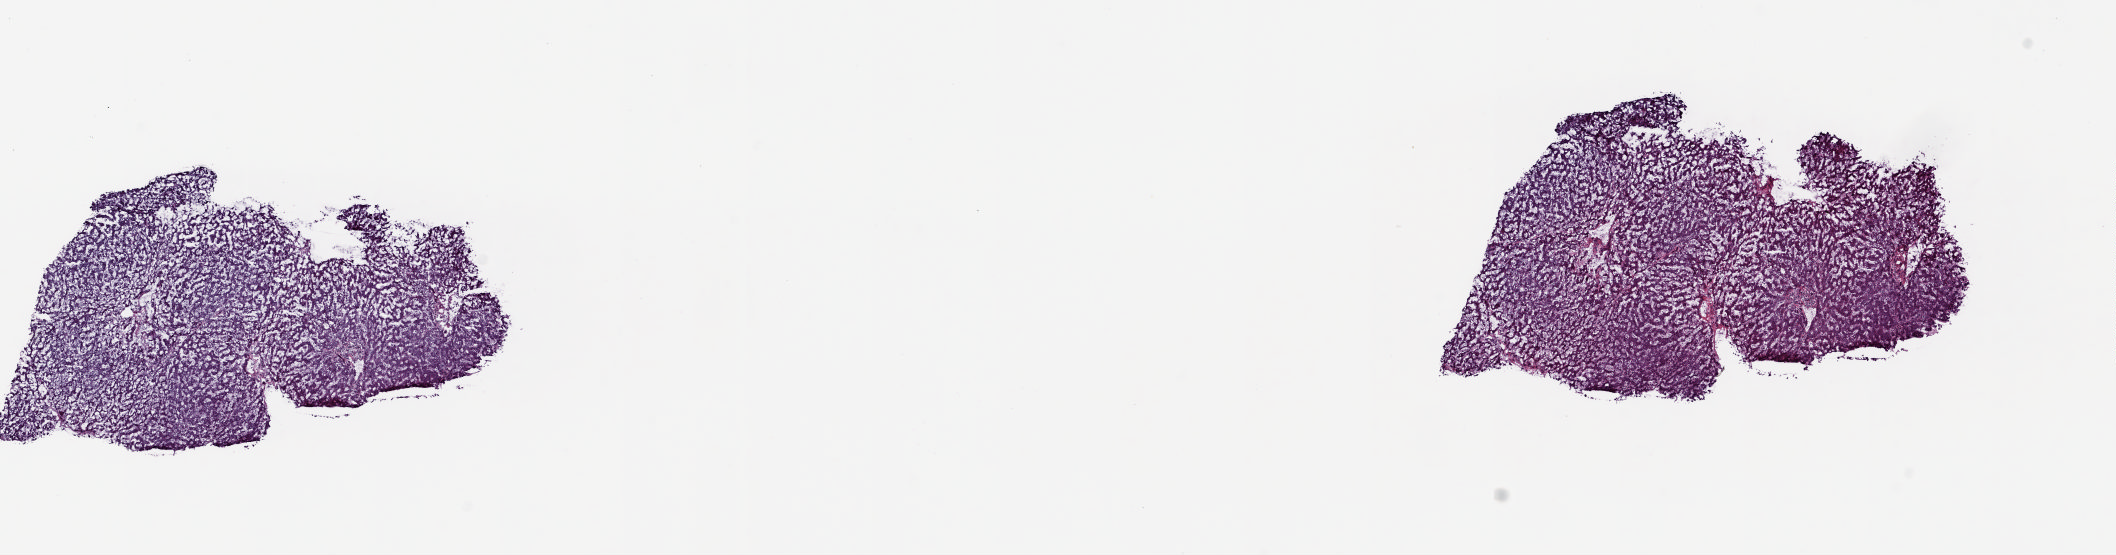
Digitized H&E tissue section (whole slide) — shown as a low-resolution overview of the whole scanned area (about 16.8 x 4.4 mm, from a 20x scan), frozen section from the top of the tissue portion, liver, solid tissue normal (non-tumour tissue) sample. Patient: female, age at initial diagnosis 62 years. Composition of this section per pathologist review: tumour cells 0%, tumour nuclei 0%, normal cells 97%, stromal cells 3%, necrosis 0%. Infiltration values recorded for this section: lymphocyte infiltration 5%, monocyte infiltration 3%, neutrophil infiltration 0%.
This section: solid tissue normal sample (biorepository sample class). Patient diagnosis: Hepatocellular carcinoma, NOS.